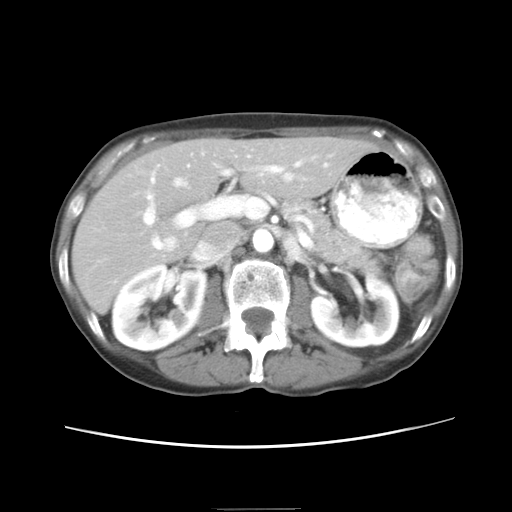
Contrast-enhanced abdominal CT, one axial slice. Slice 12 of 26 in the series (ordered by position). Reconstruction kernel STANDARD. Intravenous contrast given. Soft-tissue window (W 400 / L 40 HU). 512 × 512 image matrix, field of view 340 × 340 mm. Female patient, age 65 years. From the clinical record (not read from this slice): diagnosis: colorectal cancer liver metastases, imaged before liver resection; multiple liver metastases: no; disease in both lobes: yes; chemotherapy before resection: yes.
Outlined on this slice (manually delineated by an expert):
- hepatic veins: box from (x=146, y=155) to (x=327, y=250) px
- liver: (x=73, y=138)–(x=370, y=308)
- planned liver remnant (the part of the liver to remain after resection): (x=73, y=138)–(x=370, y=308)
- portal vein (with intrahepatic branches): (x=143, y=152)–(x=300, y=249)